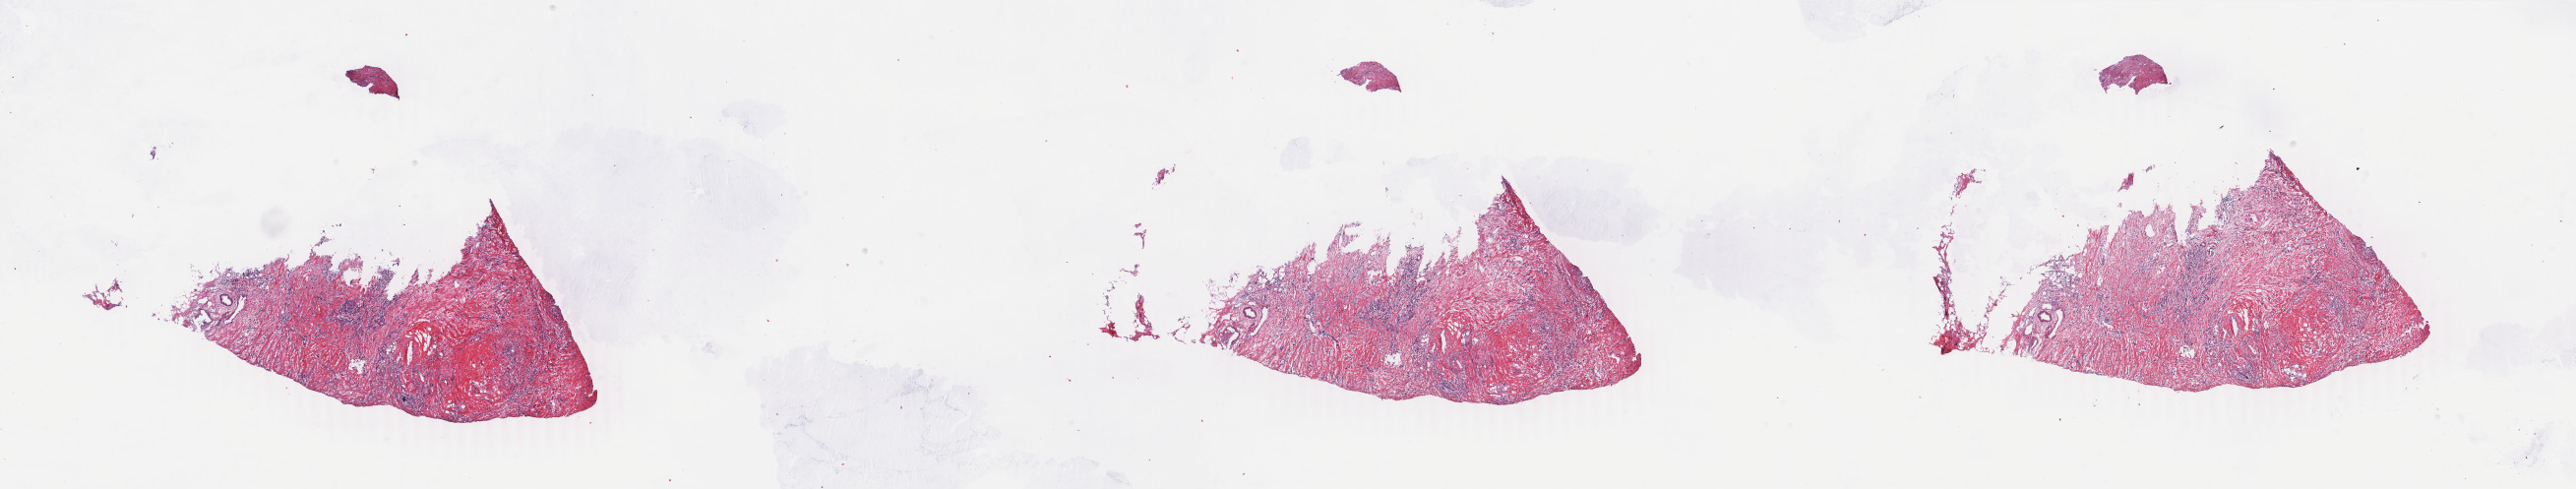
Digitized H&E-stained tissue section (whole slide) — whole scanned area (about 41.6 x 7.9 mm, from a 40x scan) shown as a low-resolution overview; frozen section from the top of the tissue portion; breast, primary tumour sample. Female patient. Pathologist review of this section (percent, as recorded): tumour cells 75%, tumour nuclei 75%, normal cells 0%, stromal cells 25%, necrosis 0%. Infiltration values recorded for this section: lymphocyte infiltration 2%, monocyte infiltration 0%, neutrophil infiltration 0%.
AJCC pathologic stage: IIIA (4th edition). Diagnosis: Lobular carcinoma, NOS.